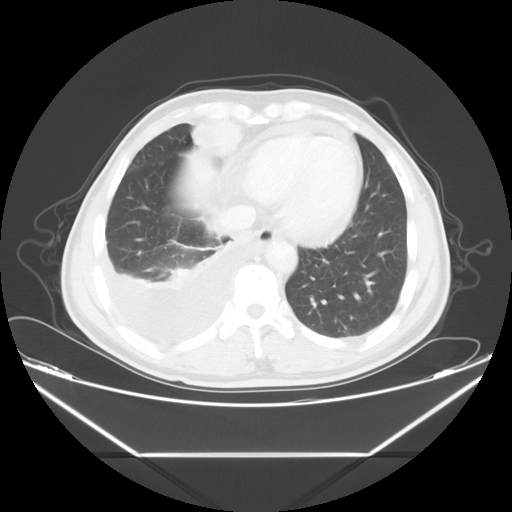
Chest CT, one axial slice; position 14 of 56 along the scan axis; reconstruction kernel STANDARD; lung window (W 1500 / L -600 HU); 512 × 512 image matrix, field of view 412 × 412 mm. Patient: male, 57 years. Case-level facts recorded for this patient, not image findings: clinical TNM (as recorded): T2 N3 M1.
Annotated regions visible in this slice (rectangle marked by the reading radiologist):
- lung tumour (recorded histology: adenocarcinoma): bounding box [x1, y1, x2, y2] px = [181, 110, 245, 156]